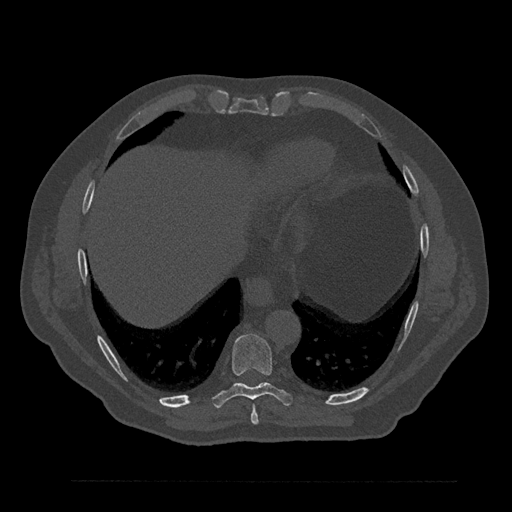
CT including the spine, one axial slice; position 405 of 797 along the scan axis; 120 kVp; bone window (W 1800 / L 400 HU); 512 × 512 image matrix, field of view 430 × 430 mm. Patient: male, 61 years. From the clinical record (not read from this slice): primary cancer: prostate.
Annotated regions visible in this slice (semi-automatically segmented with operator editing):
- T8 vertebra: box from (x=251, y=405) to (x=259, y=425) px
- T9 vertebra: (x=211, y=333)–(x=293, y=408)